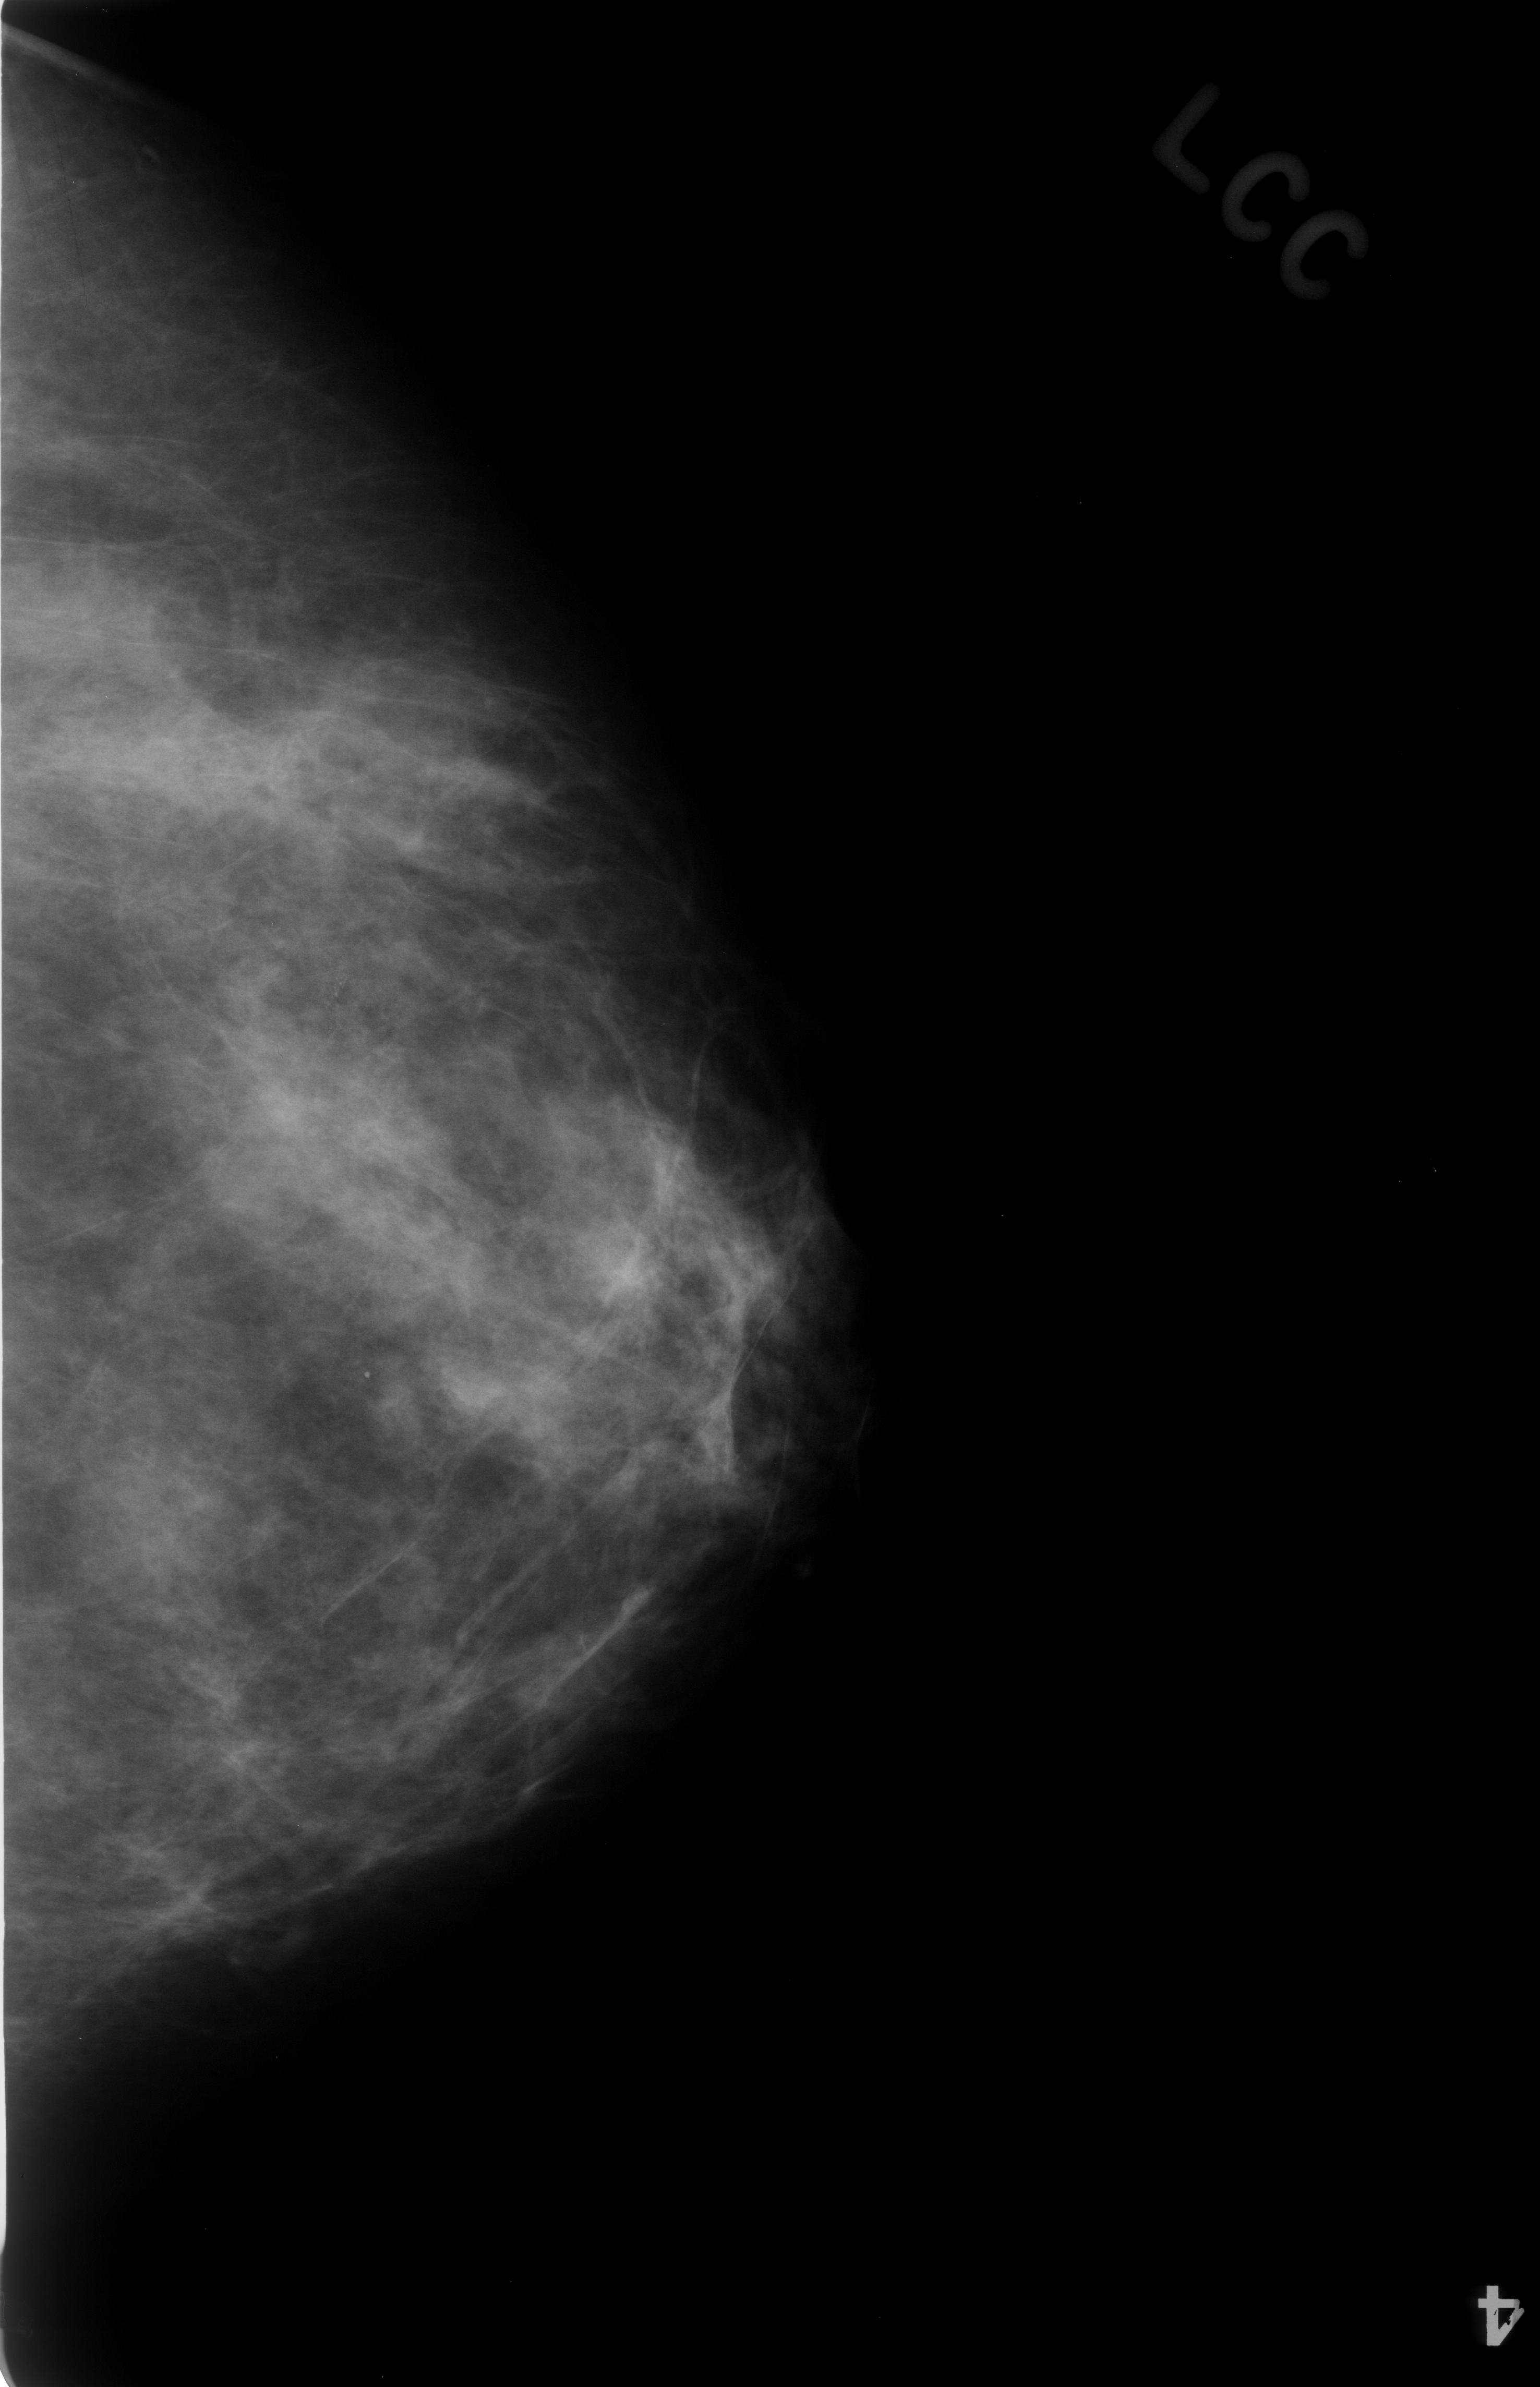
Digitized screen-film mammogram, left breast, craniocaudal (CC) view.
- Marked abnormality: calcifications, morphology amorphous, distribution clustered; BI-RADS assessment category 3; pathology (as recorded): benign.